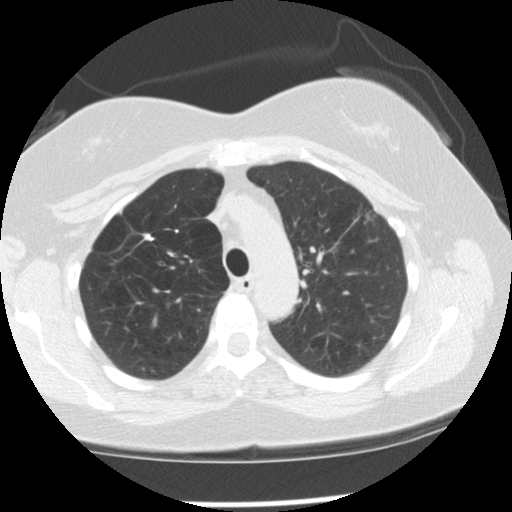
Low-dose screening chest CT, axial slice. Second annual screen. Lung window (W 1500 / L -600 HU). 120 kVp. 512 × 512 image matrix. Female participant, aged 57 years at enrolment. Former smoker at enrolment.
Expert reader's lesion annotation, bounding box [x1, y1, x2, y2] px = [352, 203, 391, 239]. Reader record for this screening exam (exam-level; its link to the box is not recorded): non-calcified nodule or mass ≥4 mm, left upper lobe, 11 × 7 mm, spiculated (stellate) margins, soft tissue attenuation, pre-existing on the prior screen: yes; interval growth: yes. Official screen result: positive, change unspecified: nodule(s) >= 4 mm or enlarging nodule(s), mass(es), or other non-specific abnormalities suspicious for lung cancer. Later outcome: lung cancer diagnosed 50 days after this screen — adenocarcinoma, NOS, left upper lobe, moderately differentiated (G2), stage IA (AJCC 6th edition), 18 mm at pathology.